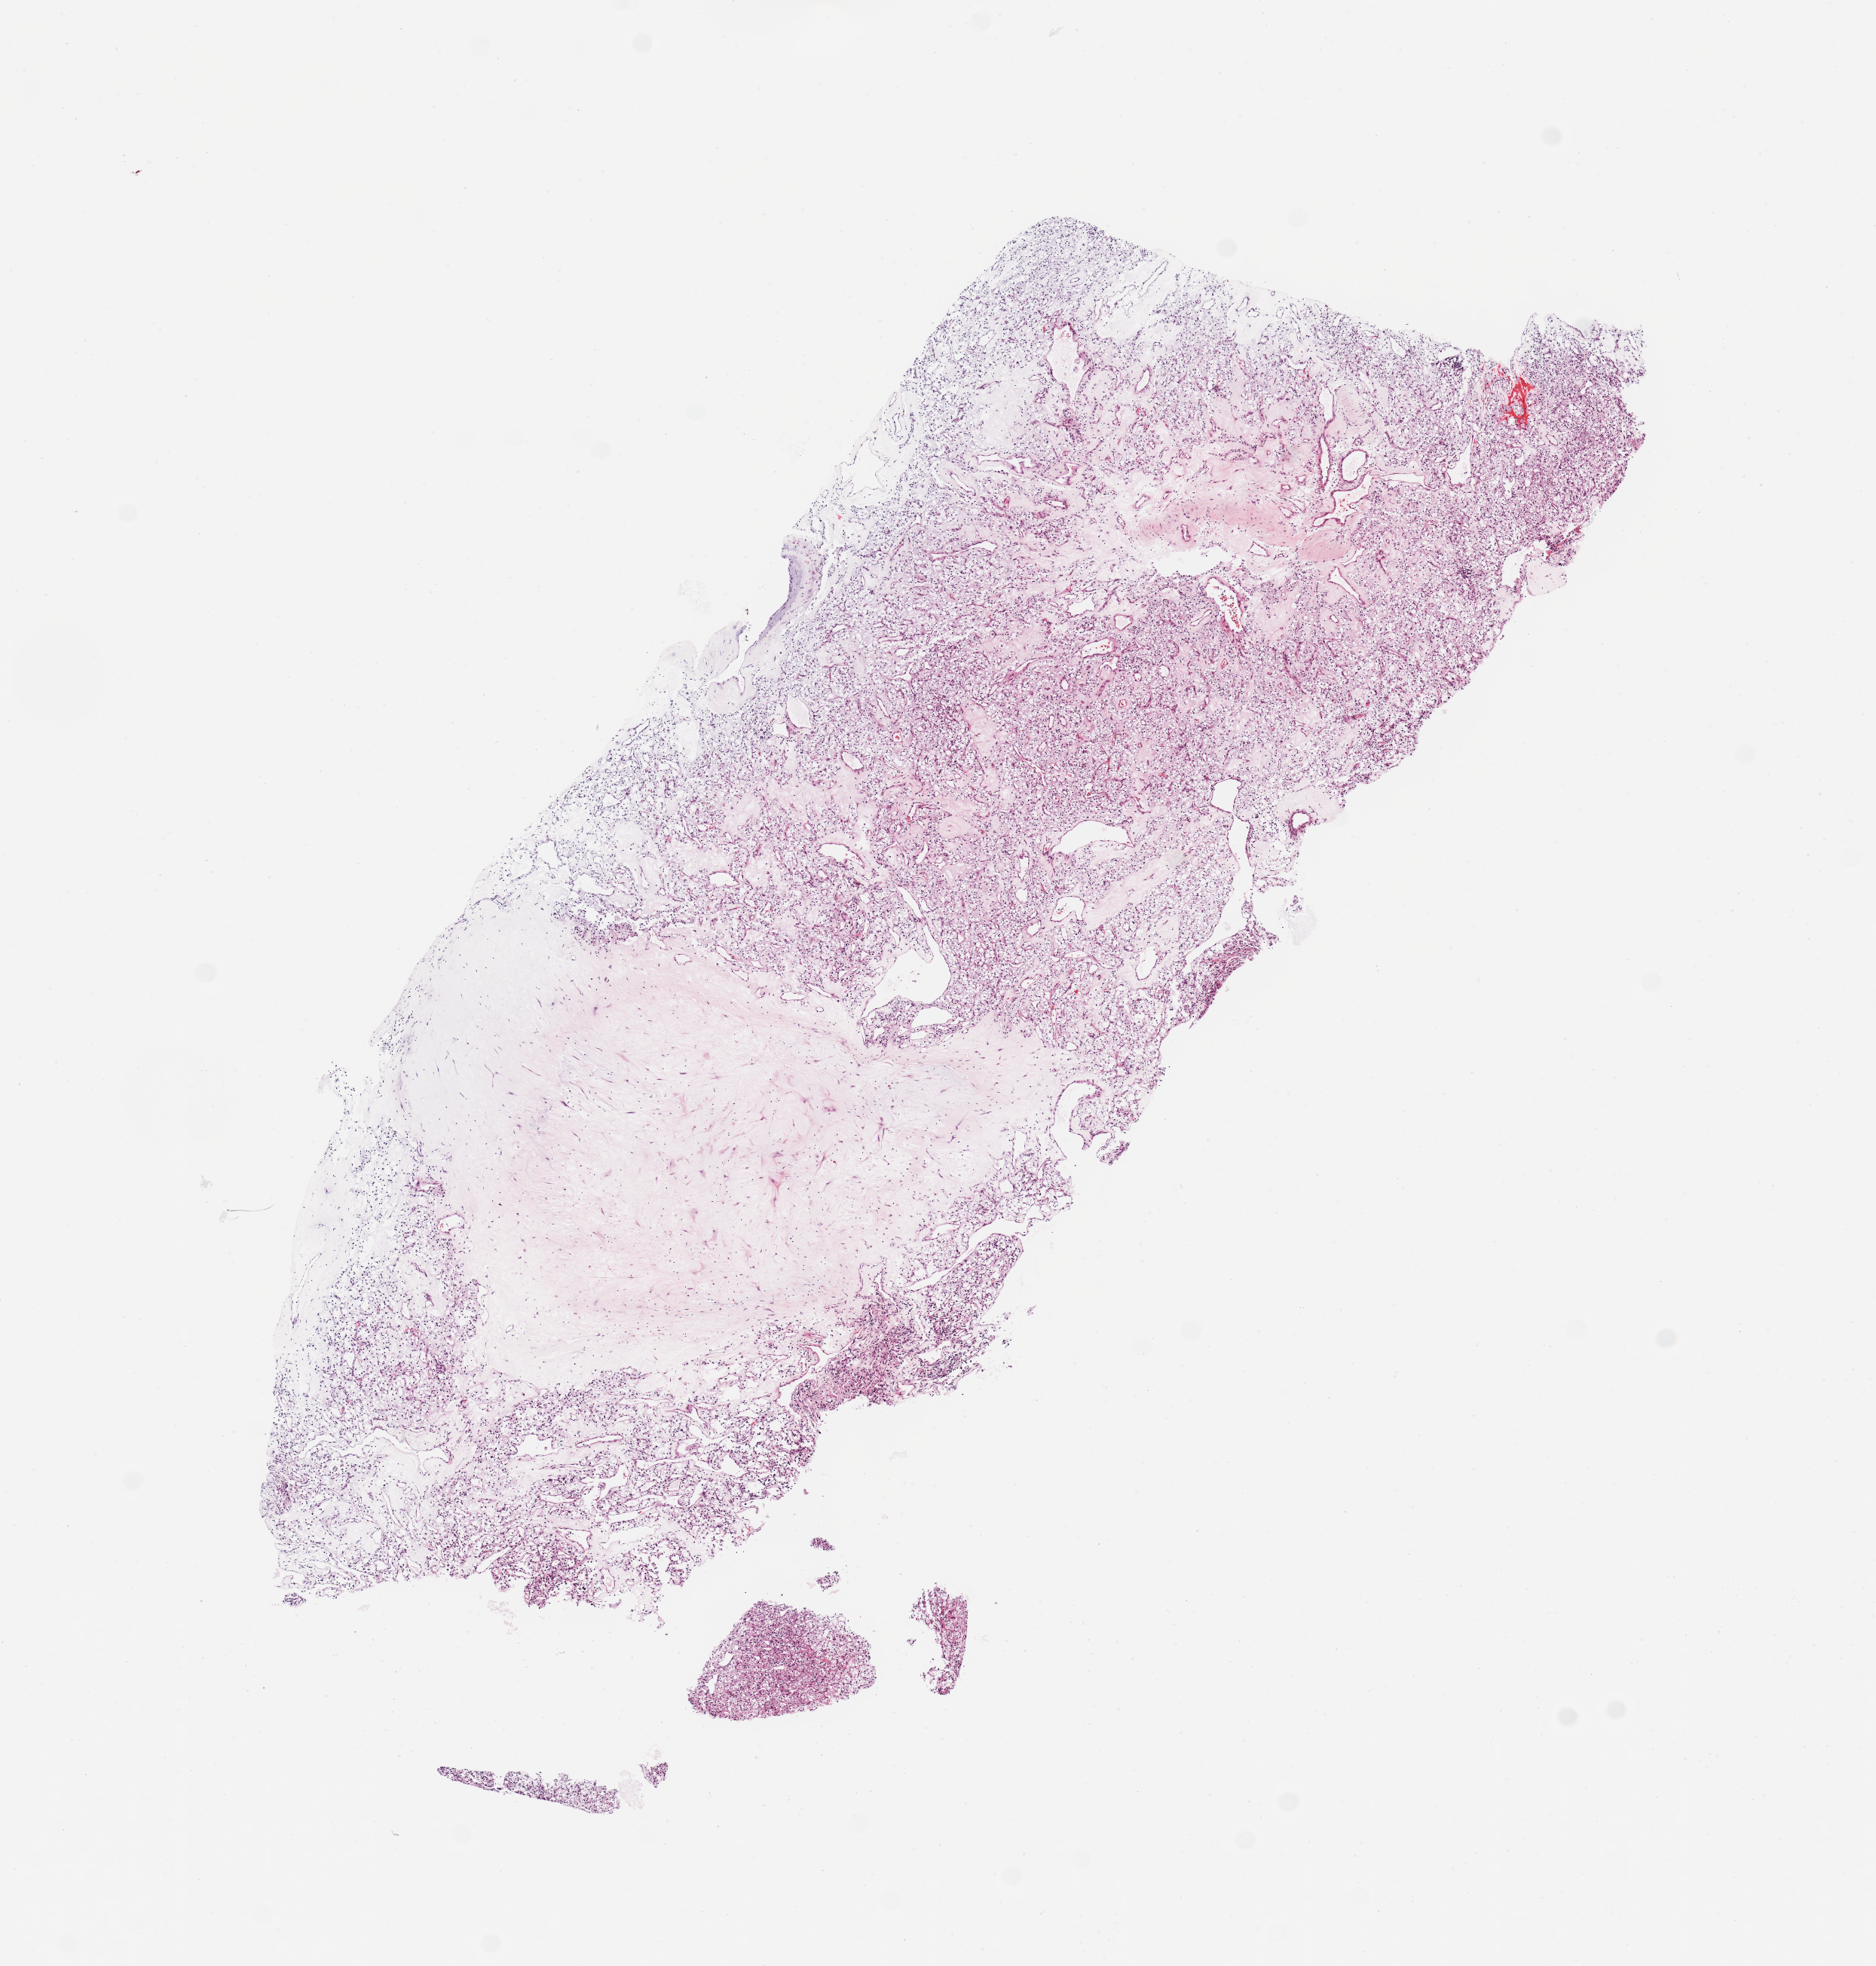
Whole-slide histology image, H&E, a low-resolution overview of the entire scanned area, about 9.8 x 10.3 mm (acquisition: 20x scan); tumour tissue sample, sampled site: kidney. Male, 56 y/o.
Histologic diagnosis: Renal cell carcinoma, NOS.